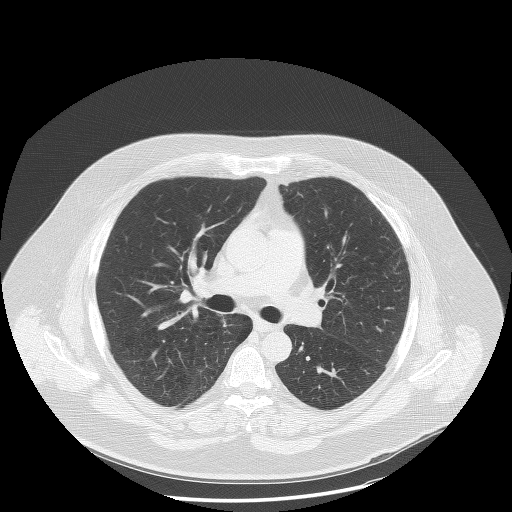
Low-dose screening chest CT, axial slice; second annual screen; lung window (W 1500 / L -600 HU); slice 50 of 132 in the series. Male participant, aged 58 years at enrolment. Former smoker at enrolment.
- Expert reader's lesion annotation, bounding box <194,302,245,343> (left, top, right, bottom; pixels).
- No non-calcified nodule or mass ≥4 mm was recorded by the screening reader at this exam.
- Lung cancer was diagnosed 471 days after this screen (after the third annual screen): squamous cell carcinoma, NOS, right upper lobe, moderately differentiated (G2), stage IA (AJCC 6th edition), 18 mm at pathology.